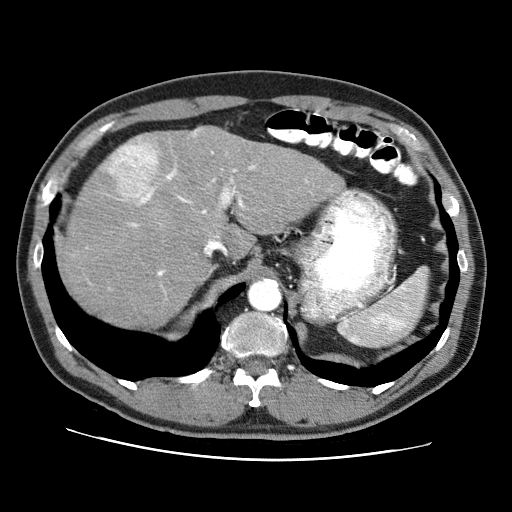
Contrast-enhanced abdominal CT (liver protocol), one axial slice; position 52 of 71 along the scan axis; reconstruction kernel STANDARD; soft-tissue window (W 400 / L 40 HU); 2.5 mm slice thickness; 512 × 512 image matrix, field of view 360 × 360 mm. From the clinical record (not read from this slice): diagnosis: hepatocellular carcinoma (patient treated with transarterial chemoembolisation; whether this scan precedes or follows treatment is not stated here); TNM stage (as recorded): Stage-II; Child-Pugh class: A; tumour size: 4.6 cm.
Structures marked on this image (semi-automatically segmented with operator editing):
- abdominal aorta: bounding box [x1, y1, x2, y2] px = [250, 281, 279, 310]
- liver parenchyma outside the tumour (the mass and vessels are separate outlines, so this box may not span the whole liver): [60, 126, 342, 326]
- mass: [108, 142, 158, 200]
- liver vessels: [132, 131, 254, 276]